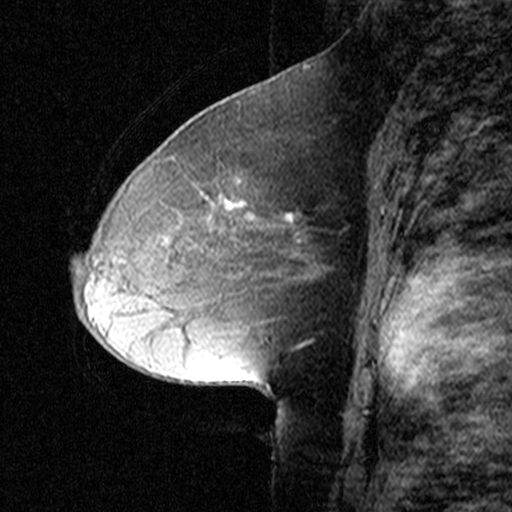
Breast MRI (dynamic contrast-enhanced), one sagittal slice. Dynamic contrast-enhanced study with each time point stored as its own series, time point 2 of 3 at this slice position (early post-contrast, ordered by acquisition time). 1.5 T. TE 4.5 ms, TR 11 ms. 512 × 512 image matrix, field of view 200 × 200 mm. Female patient, age 50 years. Case-level facts recorded for this patient, not image findings: setting: breast cancer imaged before/during neoadjuvant chemotherapy; receptor status: HR-positive, HER2-negative.
Annotated regions visible in this slice (semi-automatic segmentation, software-assisted and operator-edited):
- analysis volume of interest (the breast-tissue region the enhancement analysis was run in; not a lesion): bounding box (x1, y1, x2, y2) in pixels: (154, 164, 313, 287)
- tumour enhancement mask (voxels above the 90 % enhancement threshold inside the analysis volume of interest): (228, 200, 290, 214)